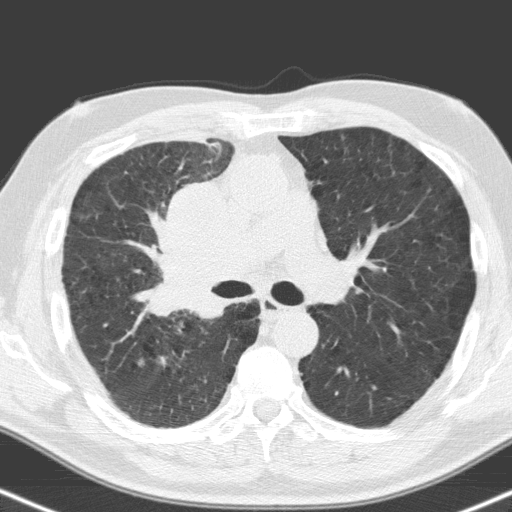
Low-dose screening chest CT, one axial slice; slice 102 of 160 in the series (ordered by position); 120 kVp; lung window (W 1500 / L -600 HU); 3.2 mm slice thickness; 512 × 512 image matrix, field of view 324 × 324 mm.
Annotated regions visible in this slice (outlined manually by an expert reader):
- lesion 1 (tumor, hilum of right lung): bounding box (x1, y1, x2, y2) in pixels: (149, 185, 258, 316)